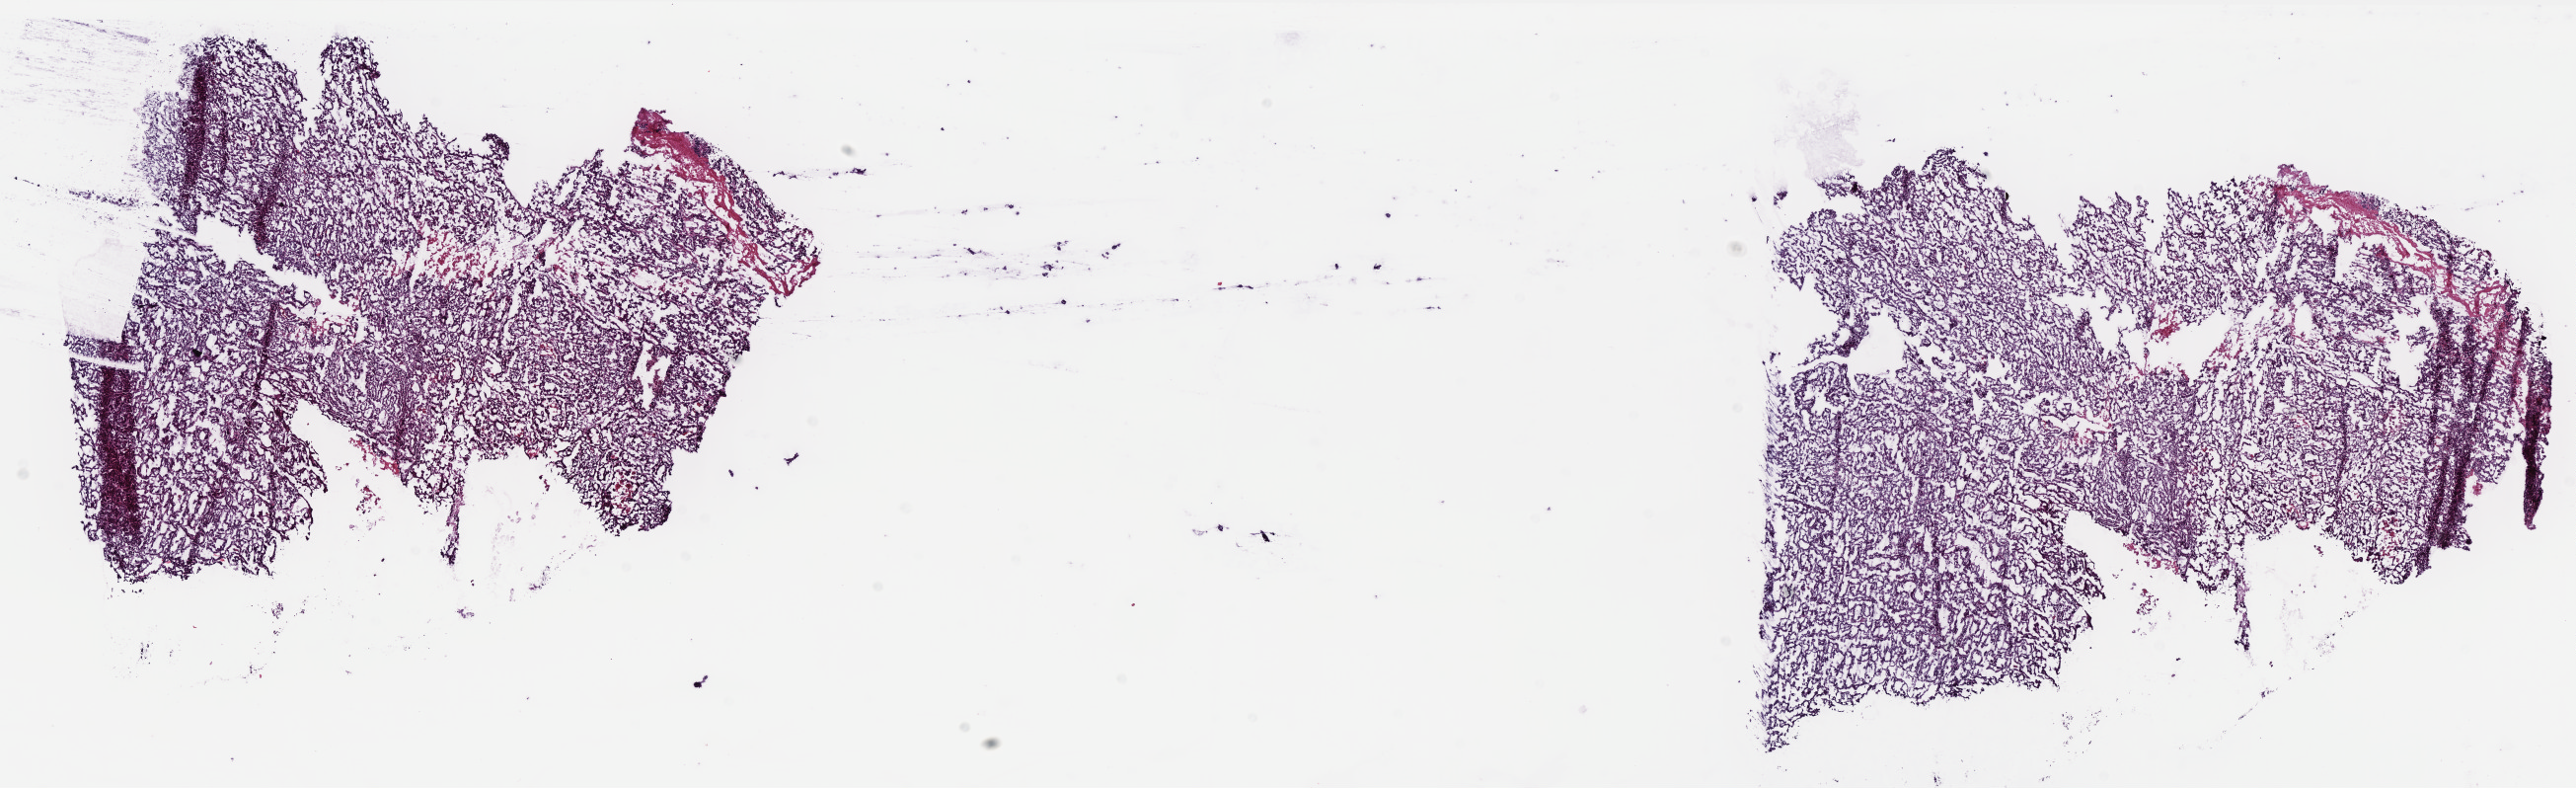
H&E-stained whole-slide image — a low-resolution overview of the entire scanned area, about 20.9 x 6.4 mm. Frozen section from the bottom of the tissue portion. Primary tumour sample from the uterus. Female, age 66 years at initial diagnosis. Histologic grade: G3 (poorly differentiated). Slide review estimates, as recorded: tumour cells 85%, tumour nuclei 95%, normal cells 0%, stromal cells 5%, necrosis 10%. Infiltration values recorded for this section: lymphocyte infiltration 0%, monocyte infiltration 0%, neutrophil infiltration 0%.
Pathologic diagnosis: Serous cystadenocarcinoma, NOS (endometrium). FIGO stage: II.